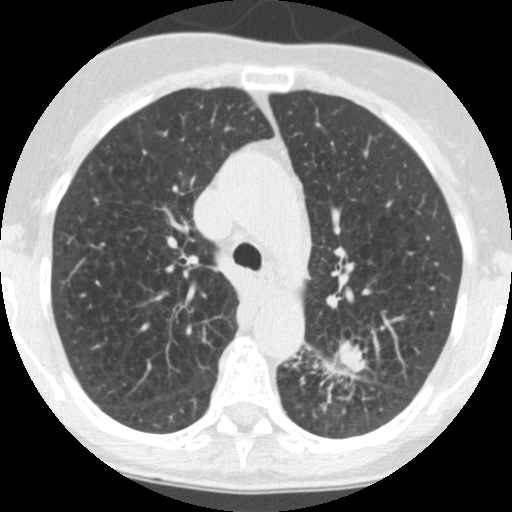
Low-dose screening chest CT, axial slice, third annual screen, lung window (W 1500 / L -600 HU), slice 51 of 171 in the series. Female participant, aged 71 years at enrolment. Current smoker at enrolment.
Lesion marked by an expert reader, bounding box [x1, y1, x2, y2] px = [295, 334, 379, 412]. The screening reader recorded 2 non-calcified nodules or masses ≥4 mm on this exam (left lower lobe, left lower lobe); which of them this box marks is not recorded. Official screen result: positive, other. Lung cancer was diagnosed 26 days after this screen: squamous cell carcinoma, NOS, left lower lobe, poorly differentiated (G3), stage IB (AJCC 6th edition), 40 mm at pathology.